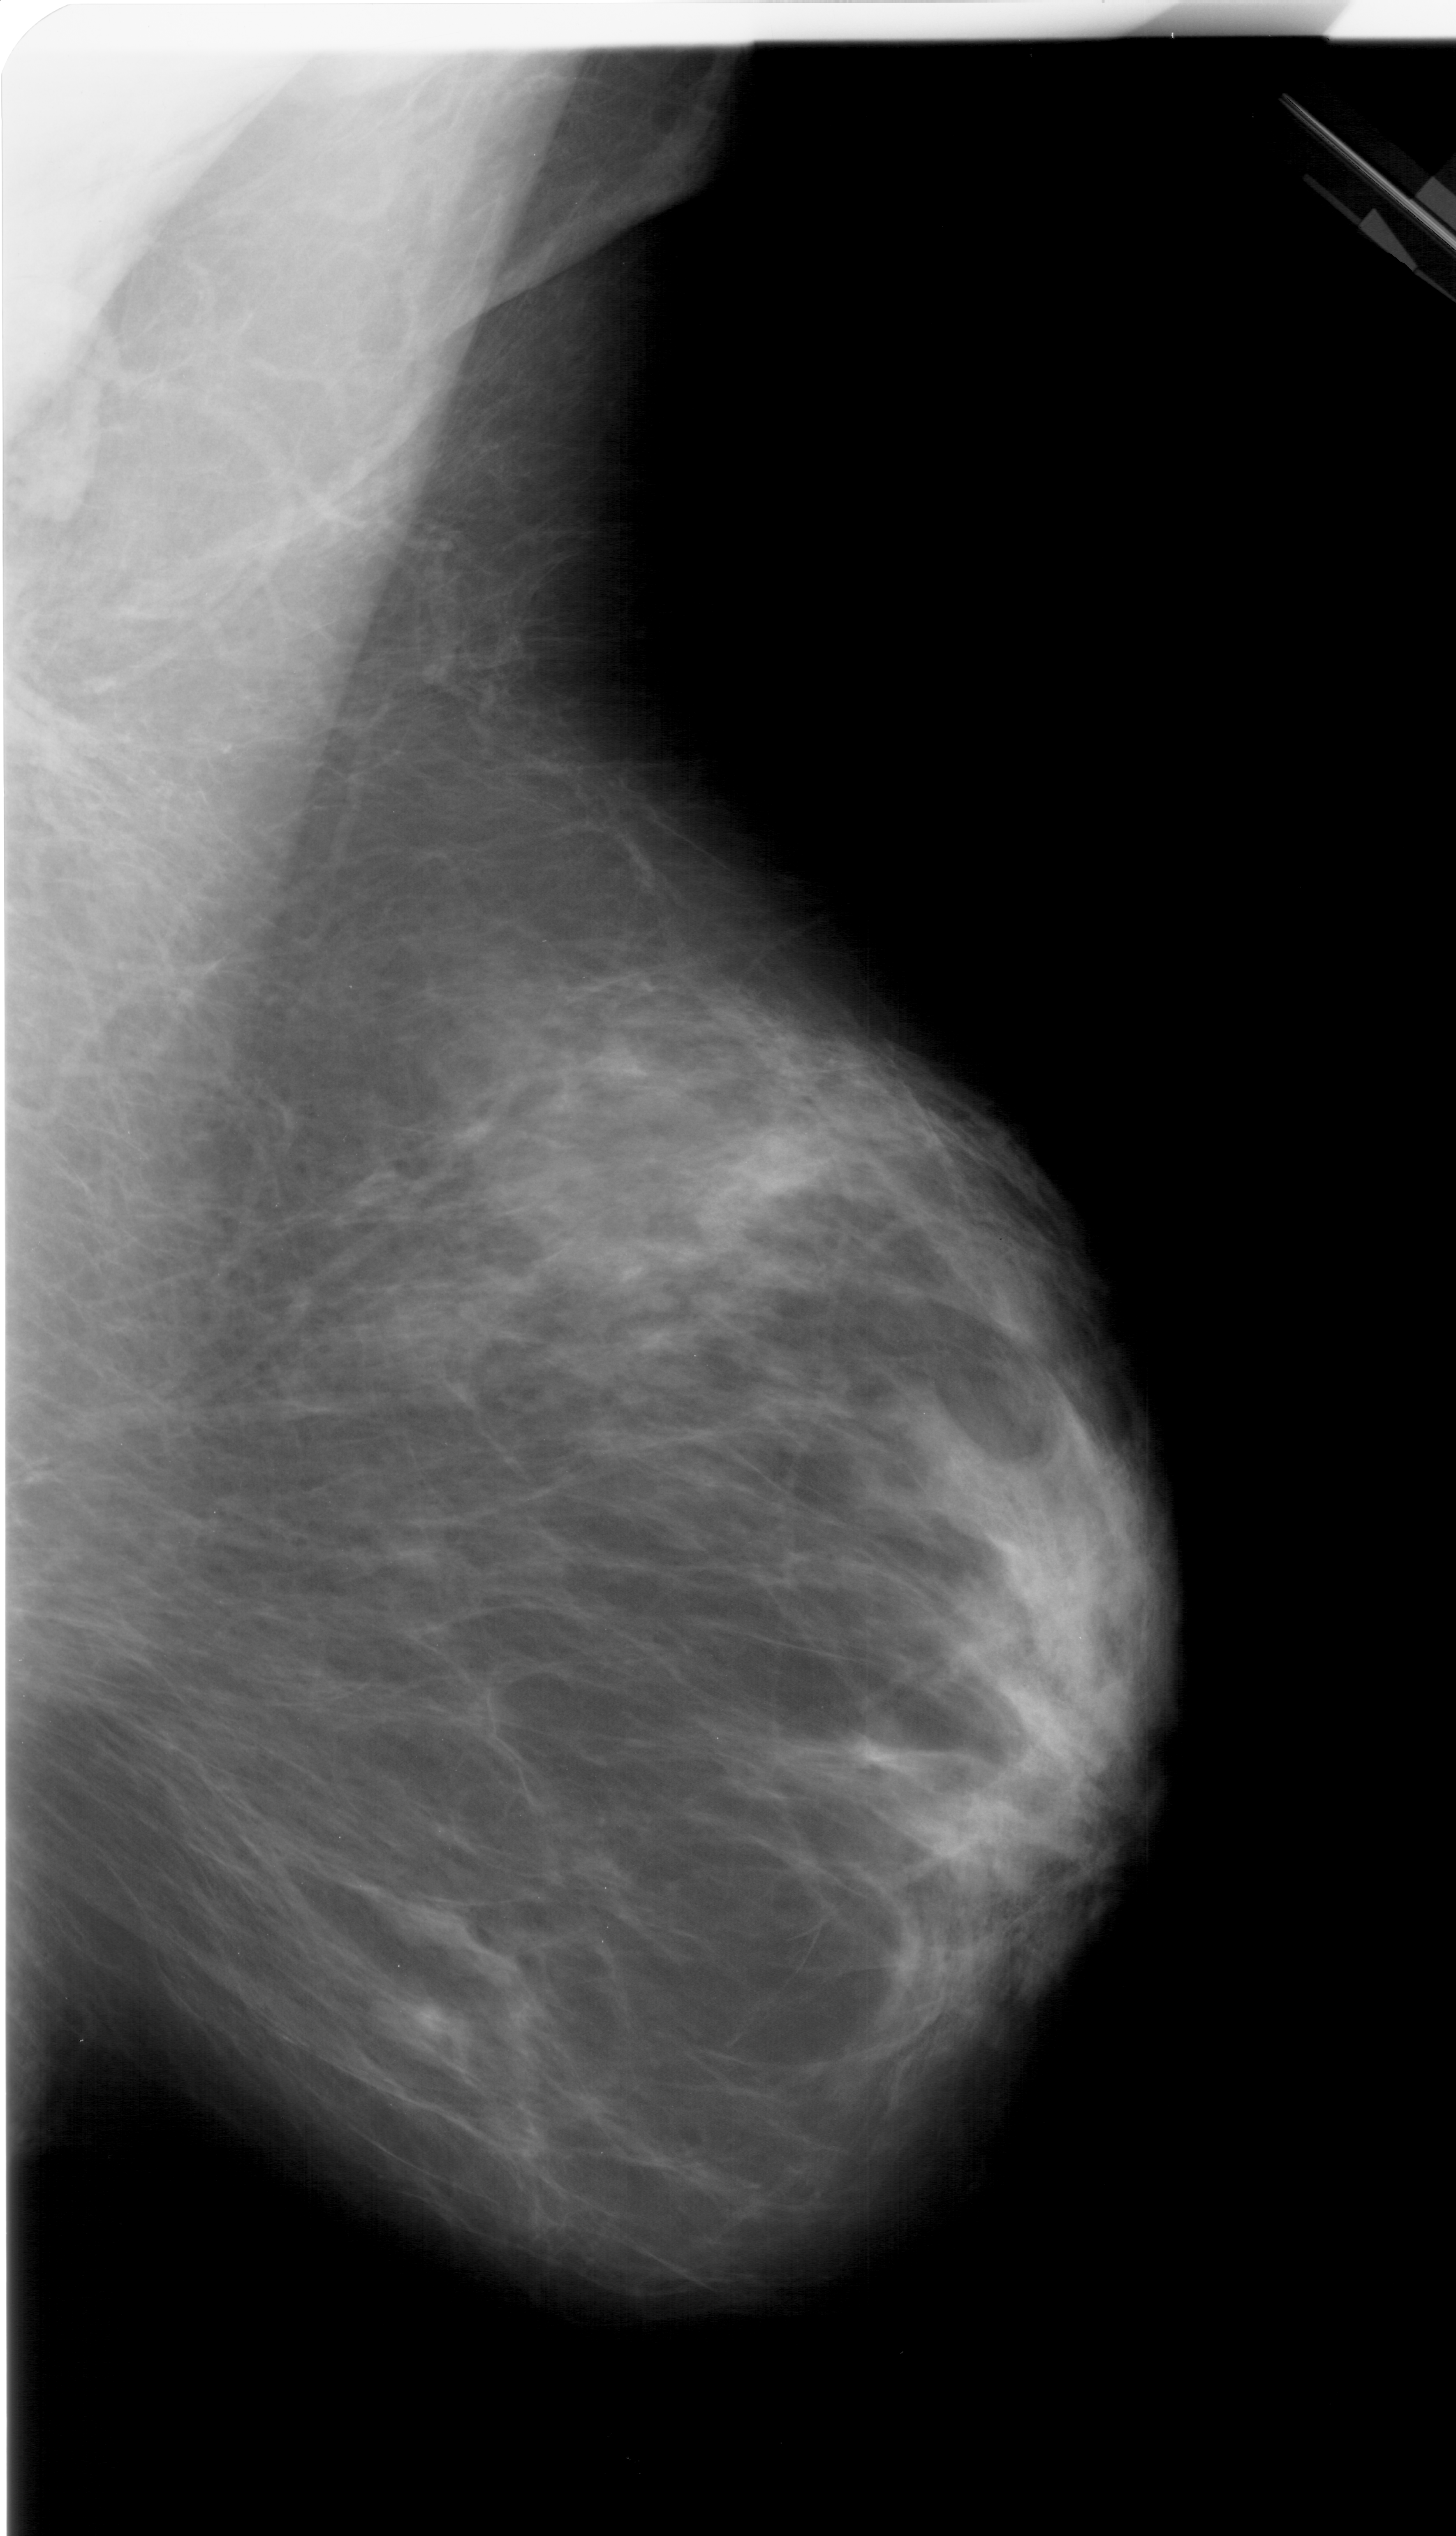
Digitized screen-film mammogram. Right breast. MLO view. Breast composition: heterogeneously dense (BI-RADS density category 3 of 4). 1456 × 2536 image matrix.
Expert-marked regions of interest on this film, with their recorded descriptors:
- mass, shape oval, margins circumscribed; BI-RADS assessment category 4; pathology (as recorded): benign: bounding box (x1, y1, x2, y2) in pixels: (368, 1979, 485, 2088)